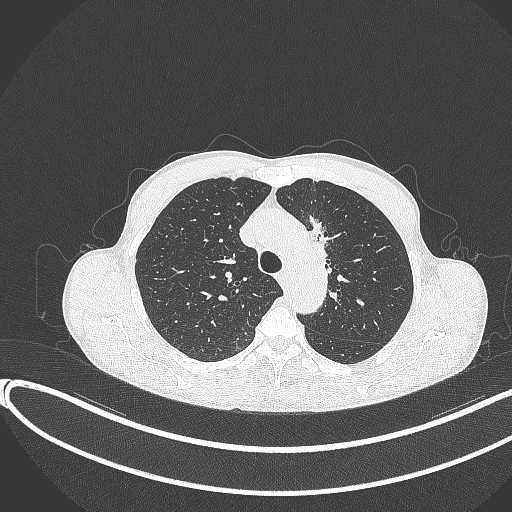
Chest CT, one axial slice. Slice 279 of 374 in the series (ordered by position). Lung window (W 1500 / L -600 HU). 1 mm slice thickness. 512 × 512 image matrix, field of view 400 × 400 mm. Patient: male, 58 years. From the clinical record (not read from this slice): clinical TNM (as recorded): T1c N1 M0.
Outlined on this slice (rectangle marked by the reading radiologist):
- lung tumour (recorded histology: adenocarcinoma): box from (x=302, y=211) to (x=344, y=275) px